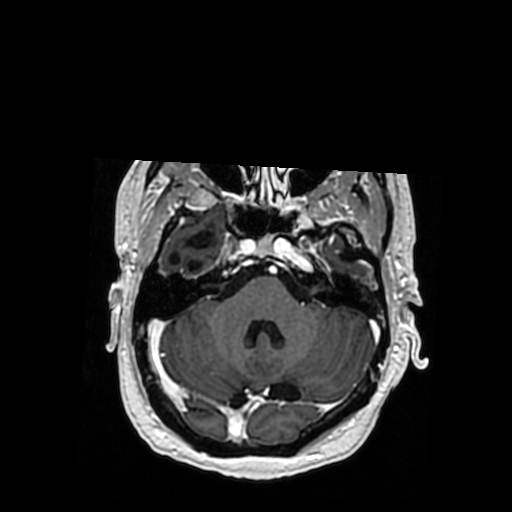
Brain MRI from a brain-tumour surgery series, one axial slice; T1-weighted post-contrast; 0.5 mm slice thickness; 512 × 512 image matrix. Case-level facts recorded for this patient, not image findings: histopathology: Oligodendroglioma; WHO grade: 3.
Outlined on this slice (outlined manually by an expert reader):
- previous resection cavity: box from (x=171, y=232) to (x=213, y=272) px